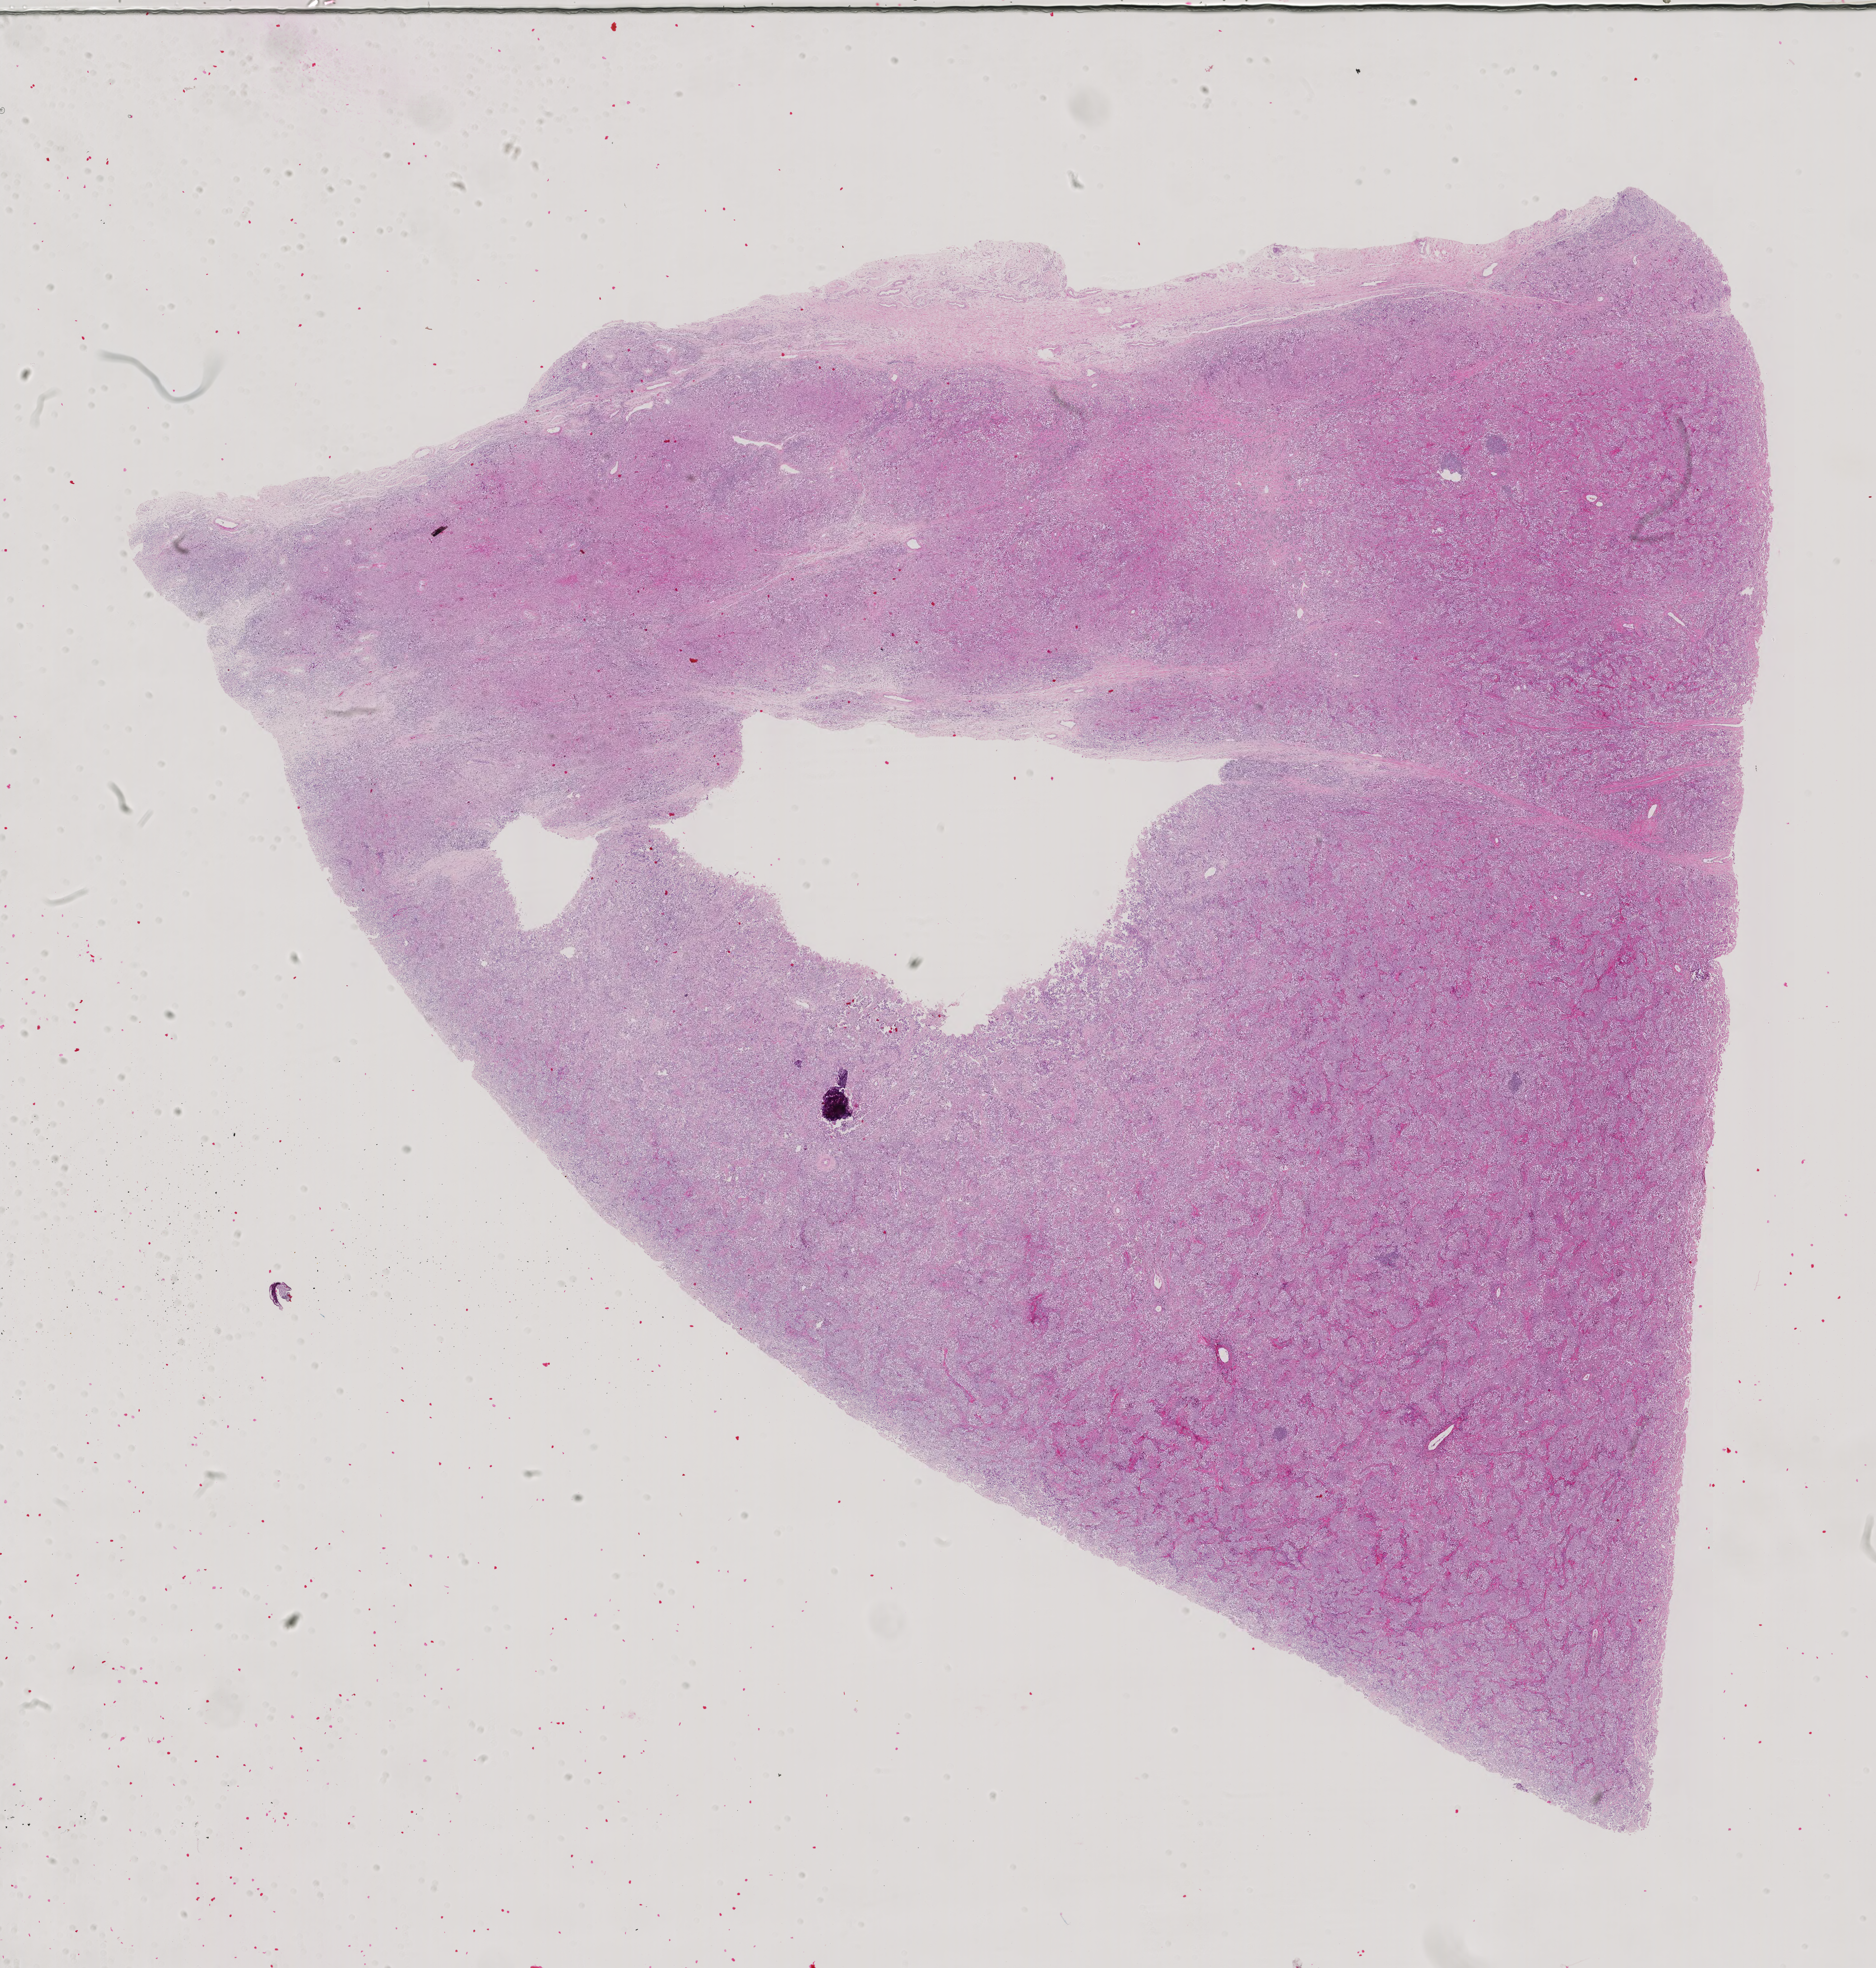
Digitized H&E tissue section (whole slide), shown as a low-resolution overview of the whole scanned area (about 21.5 x 22.5 mm), FFPE section, testis, primary tumour sample. Male patient; age at initial diagnosis 48 years.
TNM: T2 NX M0. Pathologic diagnosis: Seminoma, NOS. AJCC pathologic stage: IB (6th edition).